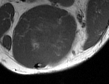
MRI of an extremity soft-tissue mass, one axial slice. Slice 37 of 50 in the series (ordered by position). MR volume resampled by the dataset authors to the PET/CT grid (not the native acquisition matrix). 3.27 mm slice thickness. 109 × 84 image matrix. Male patient. Case-level facts recorded for this patient, not image findings: histological type: synovial sarcoma; site of the primary tumour: left poplietal fossa.
Structures marked on this image (expert contour drawn on MRI and transferred to this co-registered scan by the dataset authors):
- gross tumour volume (mass): bounding box [x1, y1, x2, y2] px = [27, 21, 67, 63]